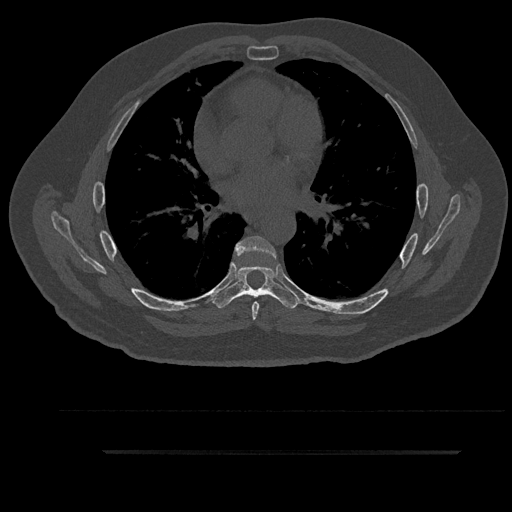
CT including the spine, one axial slice; slice 548 of 797 in the series (ordered by position); 120 kVp; bone window (W 1800 / L 400 HU); 512 × 512 image matrix. Patient: male, 63 years. Case-level facts recorded for this patient, not image findings: primary cancer: renal; vertebrae with lytic lesions (as recorded): T8.
Outlined on this slice (semi-automatically segmented with operator editing):
- T6 vertebra: bounding box <235,236,276,320> (left, top, right, bottom; pixels)
- T7 vertebra: <212,265,298,309>